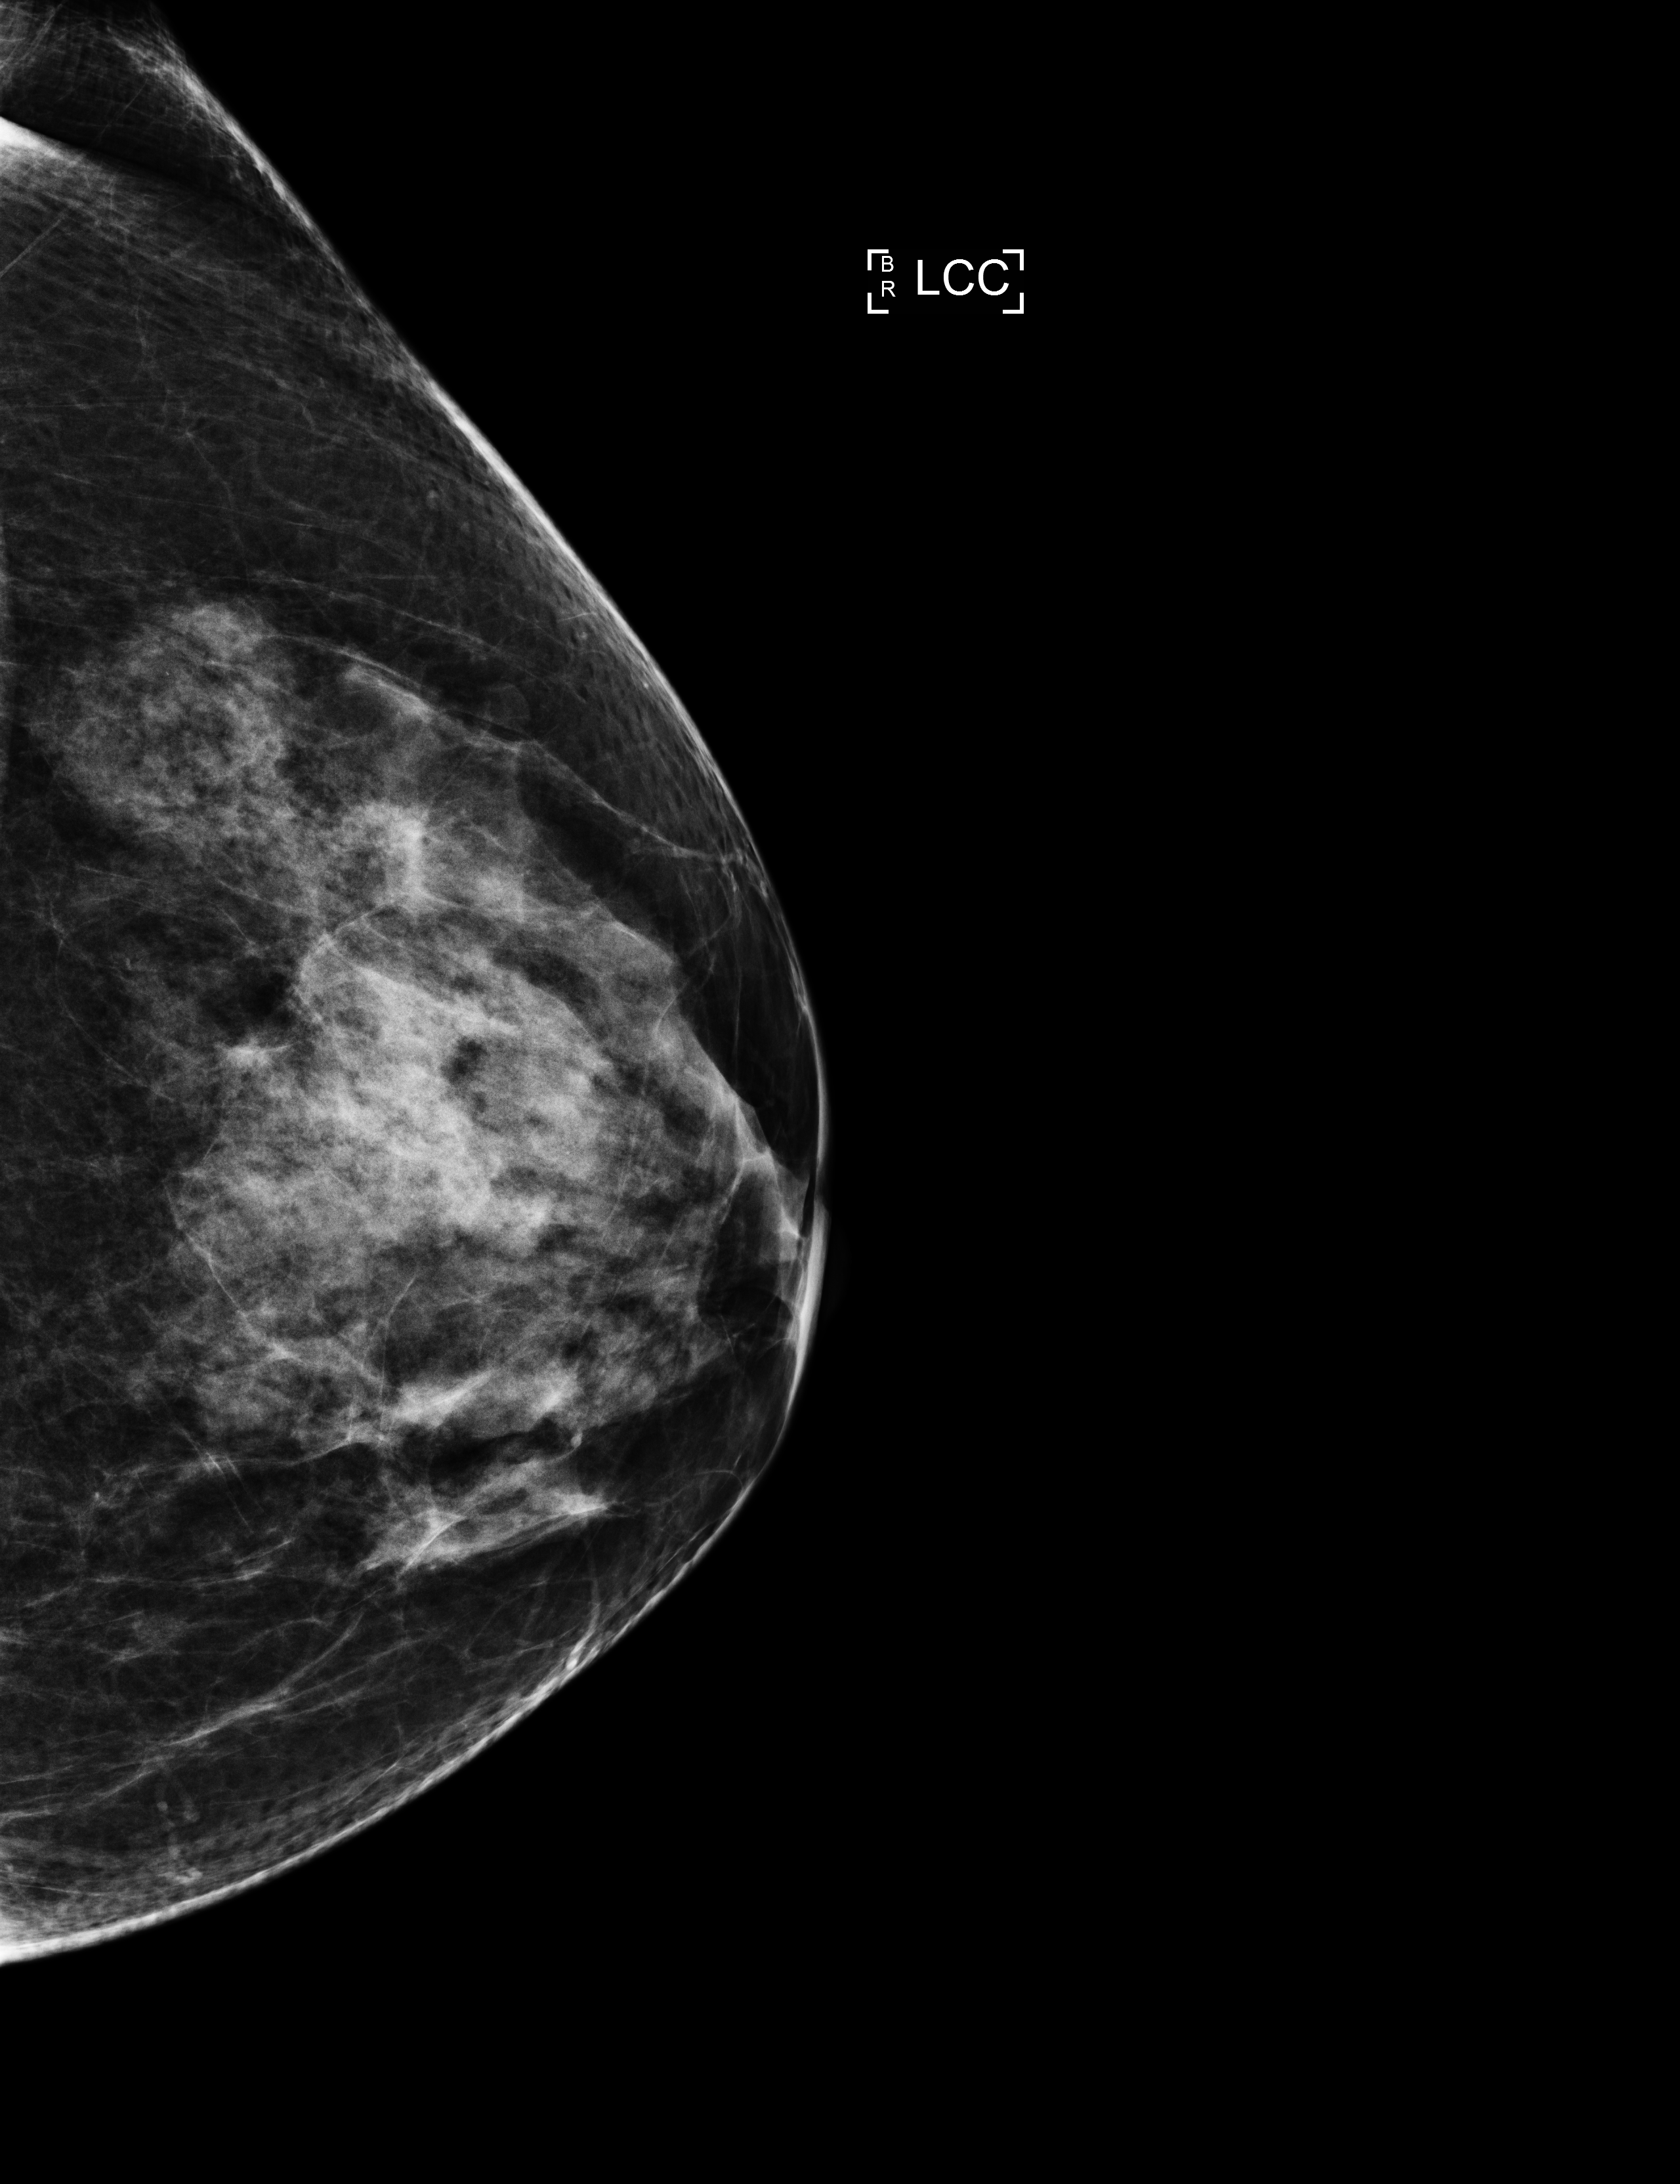
Annual screening mammography examination. Female patient, age 67 years.
Image type: full-field digital mammogram. Breast: left. Projection: cranio-caudal projection.